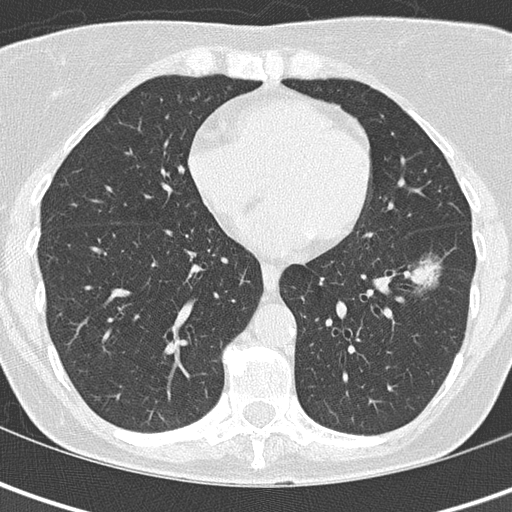
Low-dose screening chest CT, one axial slice; slice 59 of 149 in the series (ordered by position); reconstruction kernel B50f; 120 kVp; lung window (W 1500 / L -600 HU); 512 × 512 image matrix, field of view 280 × 280 mm.
Structures marked on this image (outlined manually by an expert reader):
- lesion 1 (tumor, lower lobe of left lung): bounding box [x1, y1, x2, y2] px = [407, 260, 438, 289]